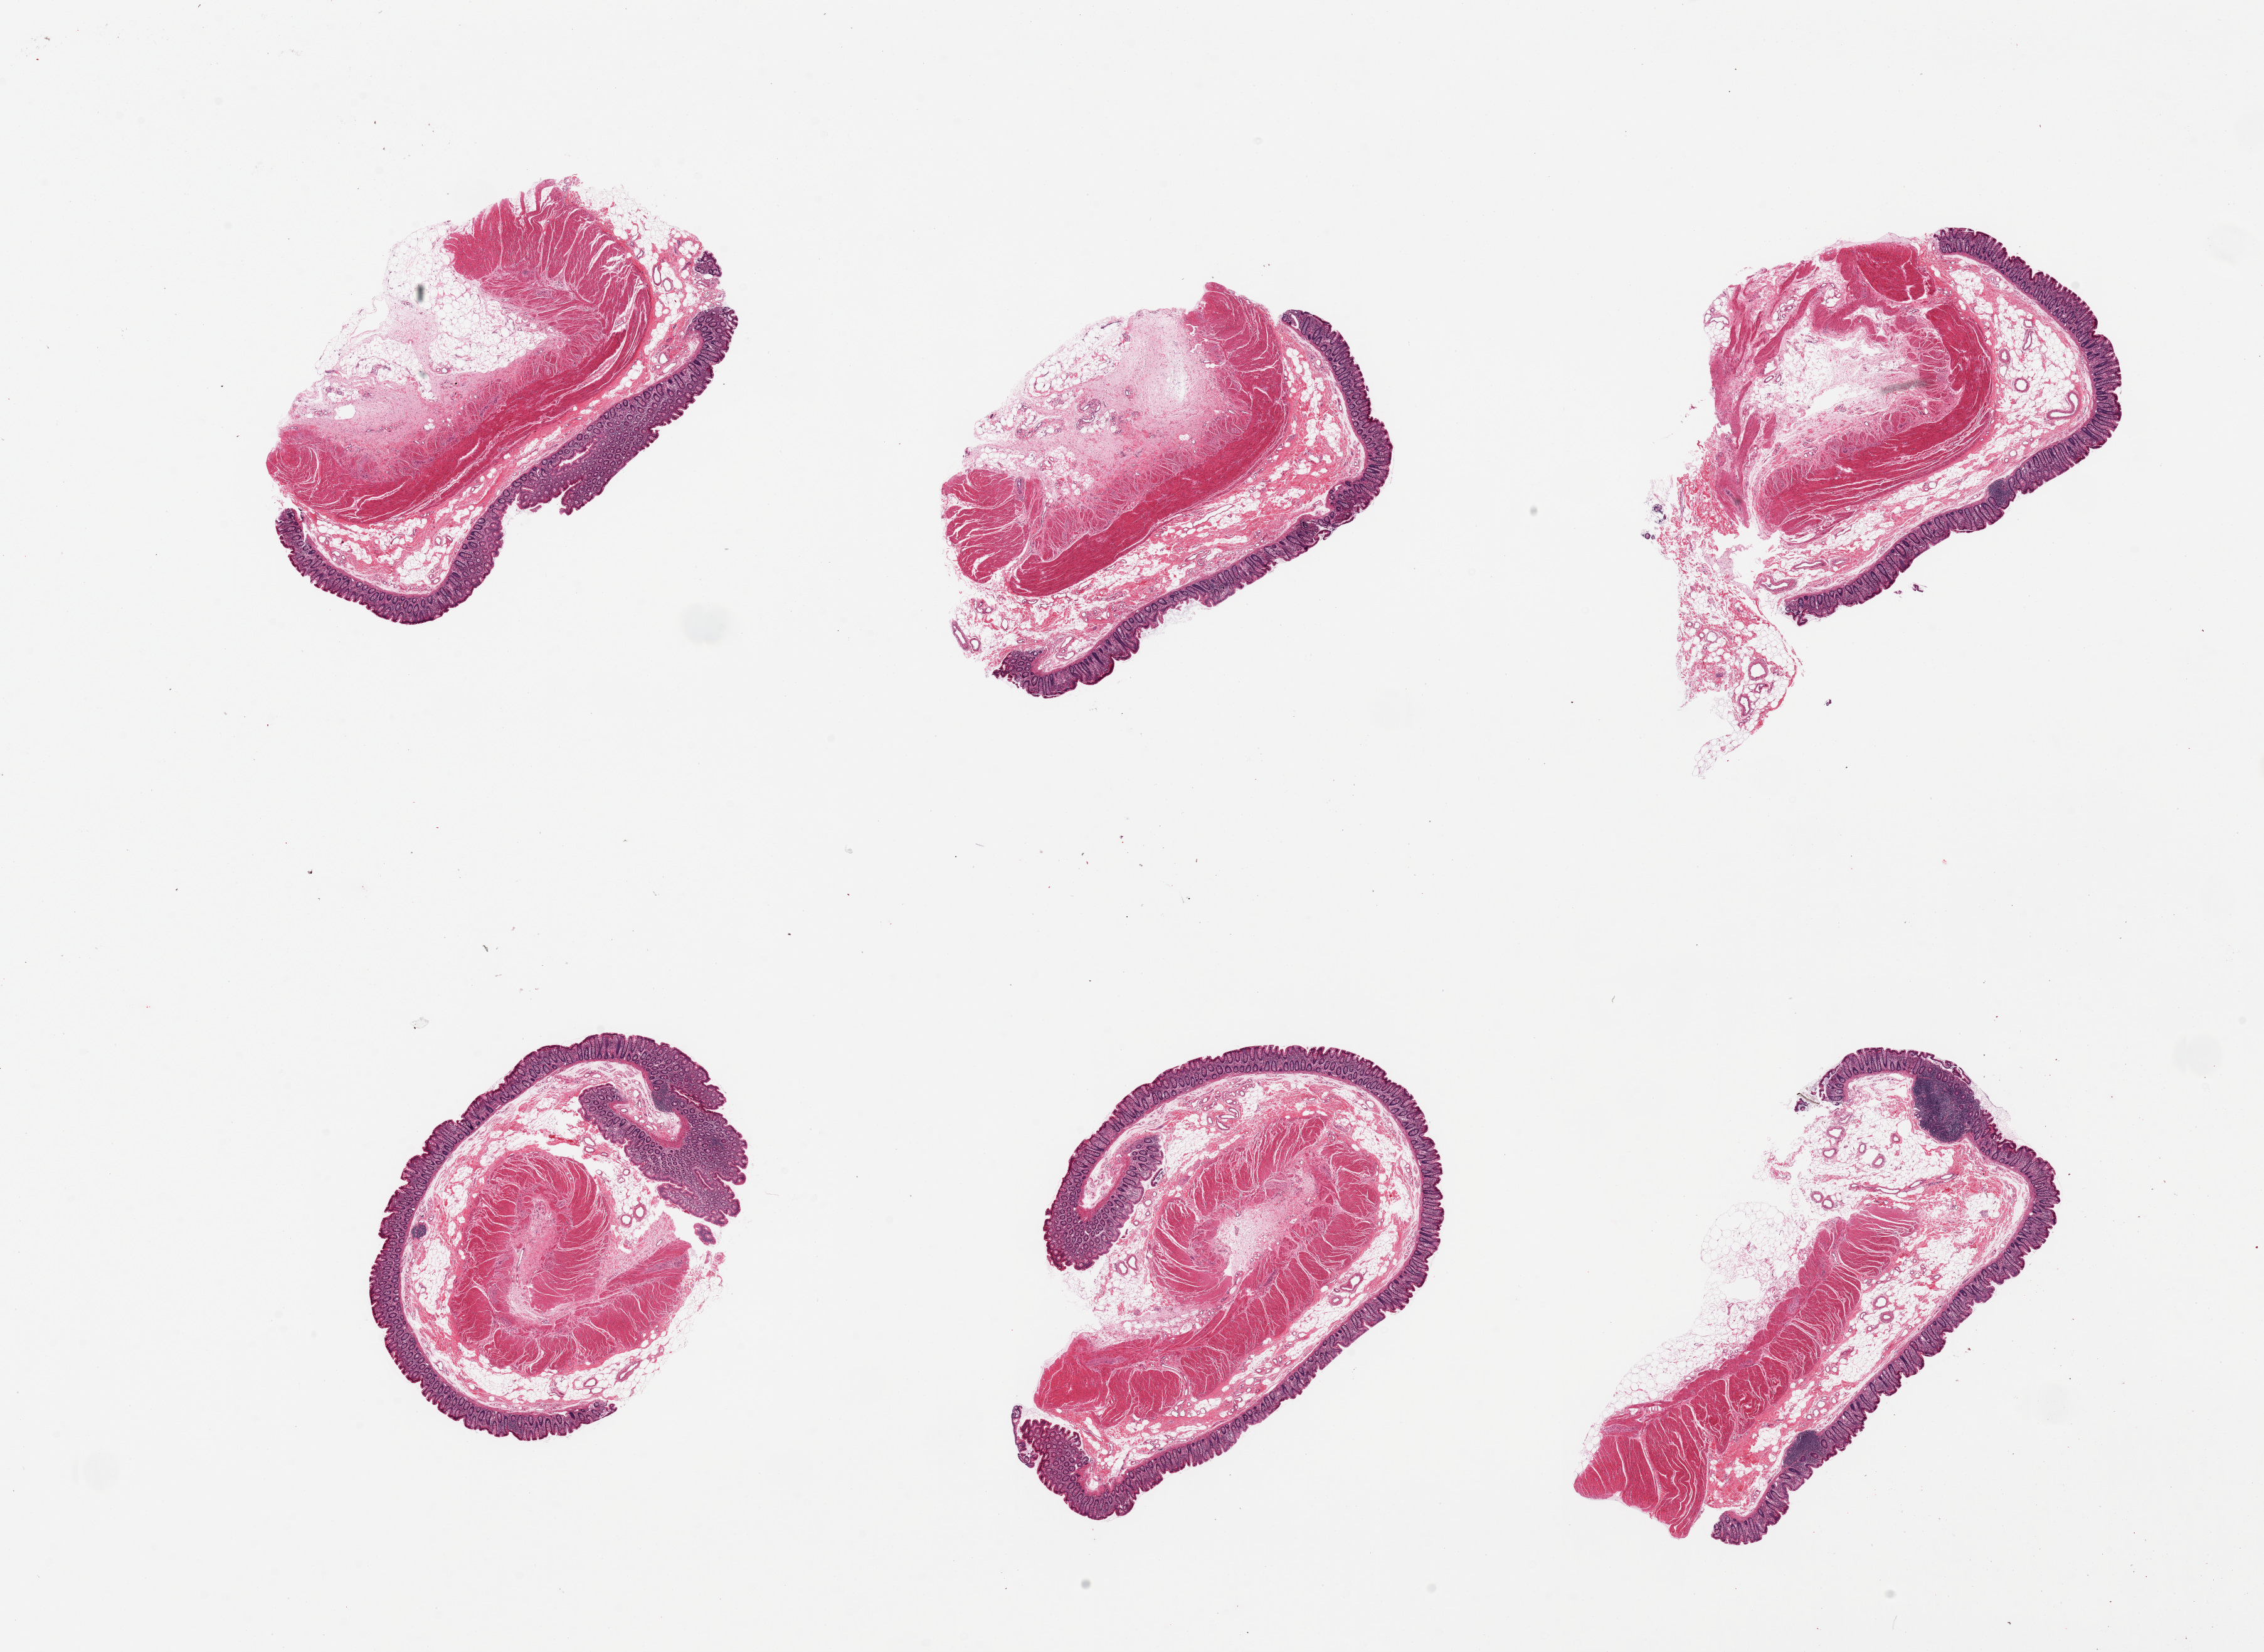
Digitized hematoxylin and eosin (H&E)-stained section, brightfield, low-resolution overview of the scanned area, about 28.5 x 20.8 mm. PAXgene-fixed paraffin-embedded (PFPE) section. Sampled site (target tissue): transverse colon. Donor tissue sample. Donor: male.
Review note (as recorded): 6 pieces: all well dissected full thickness.